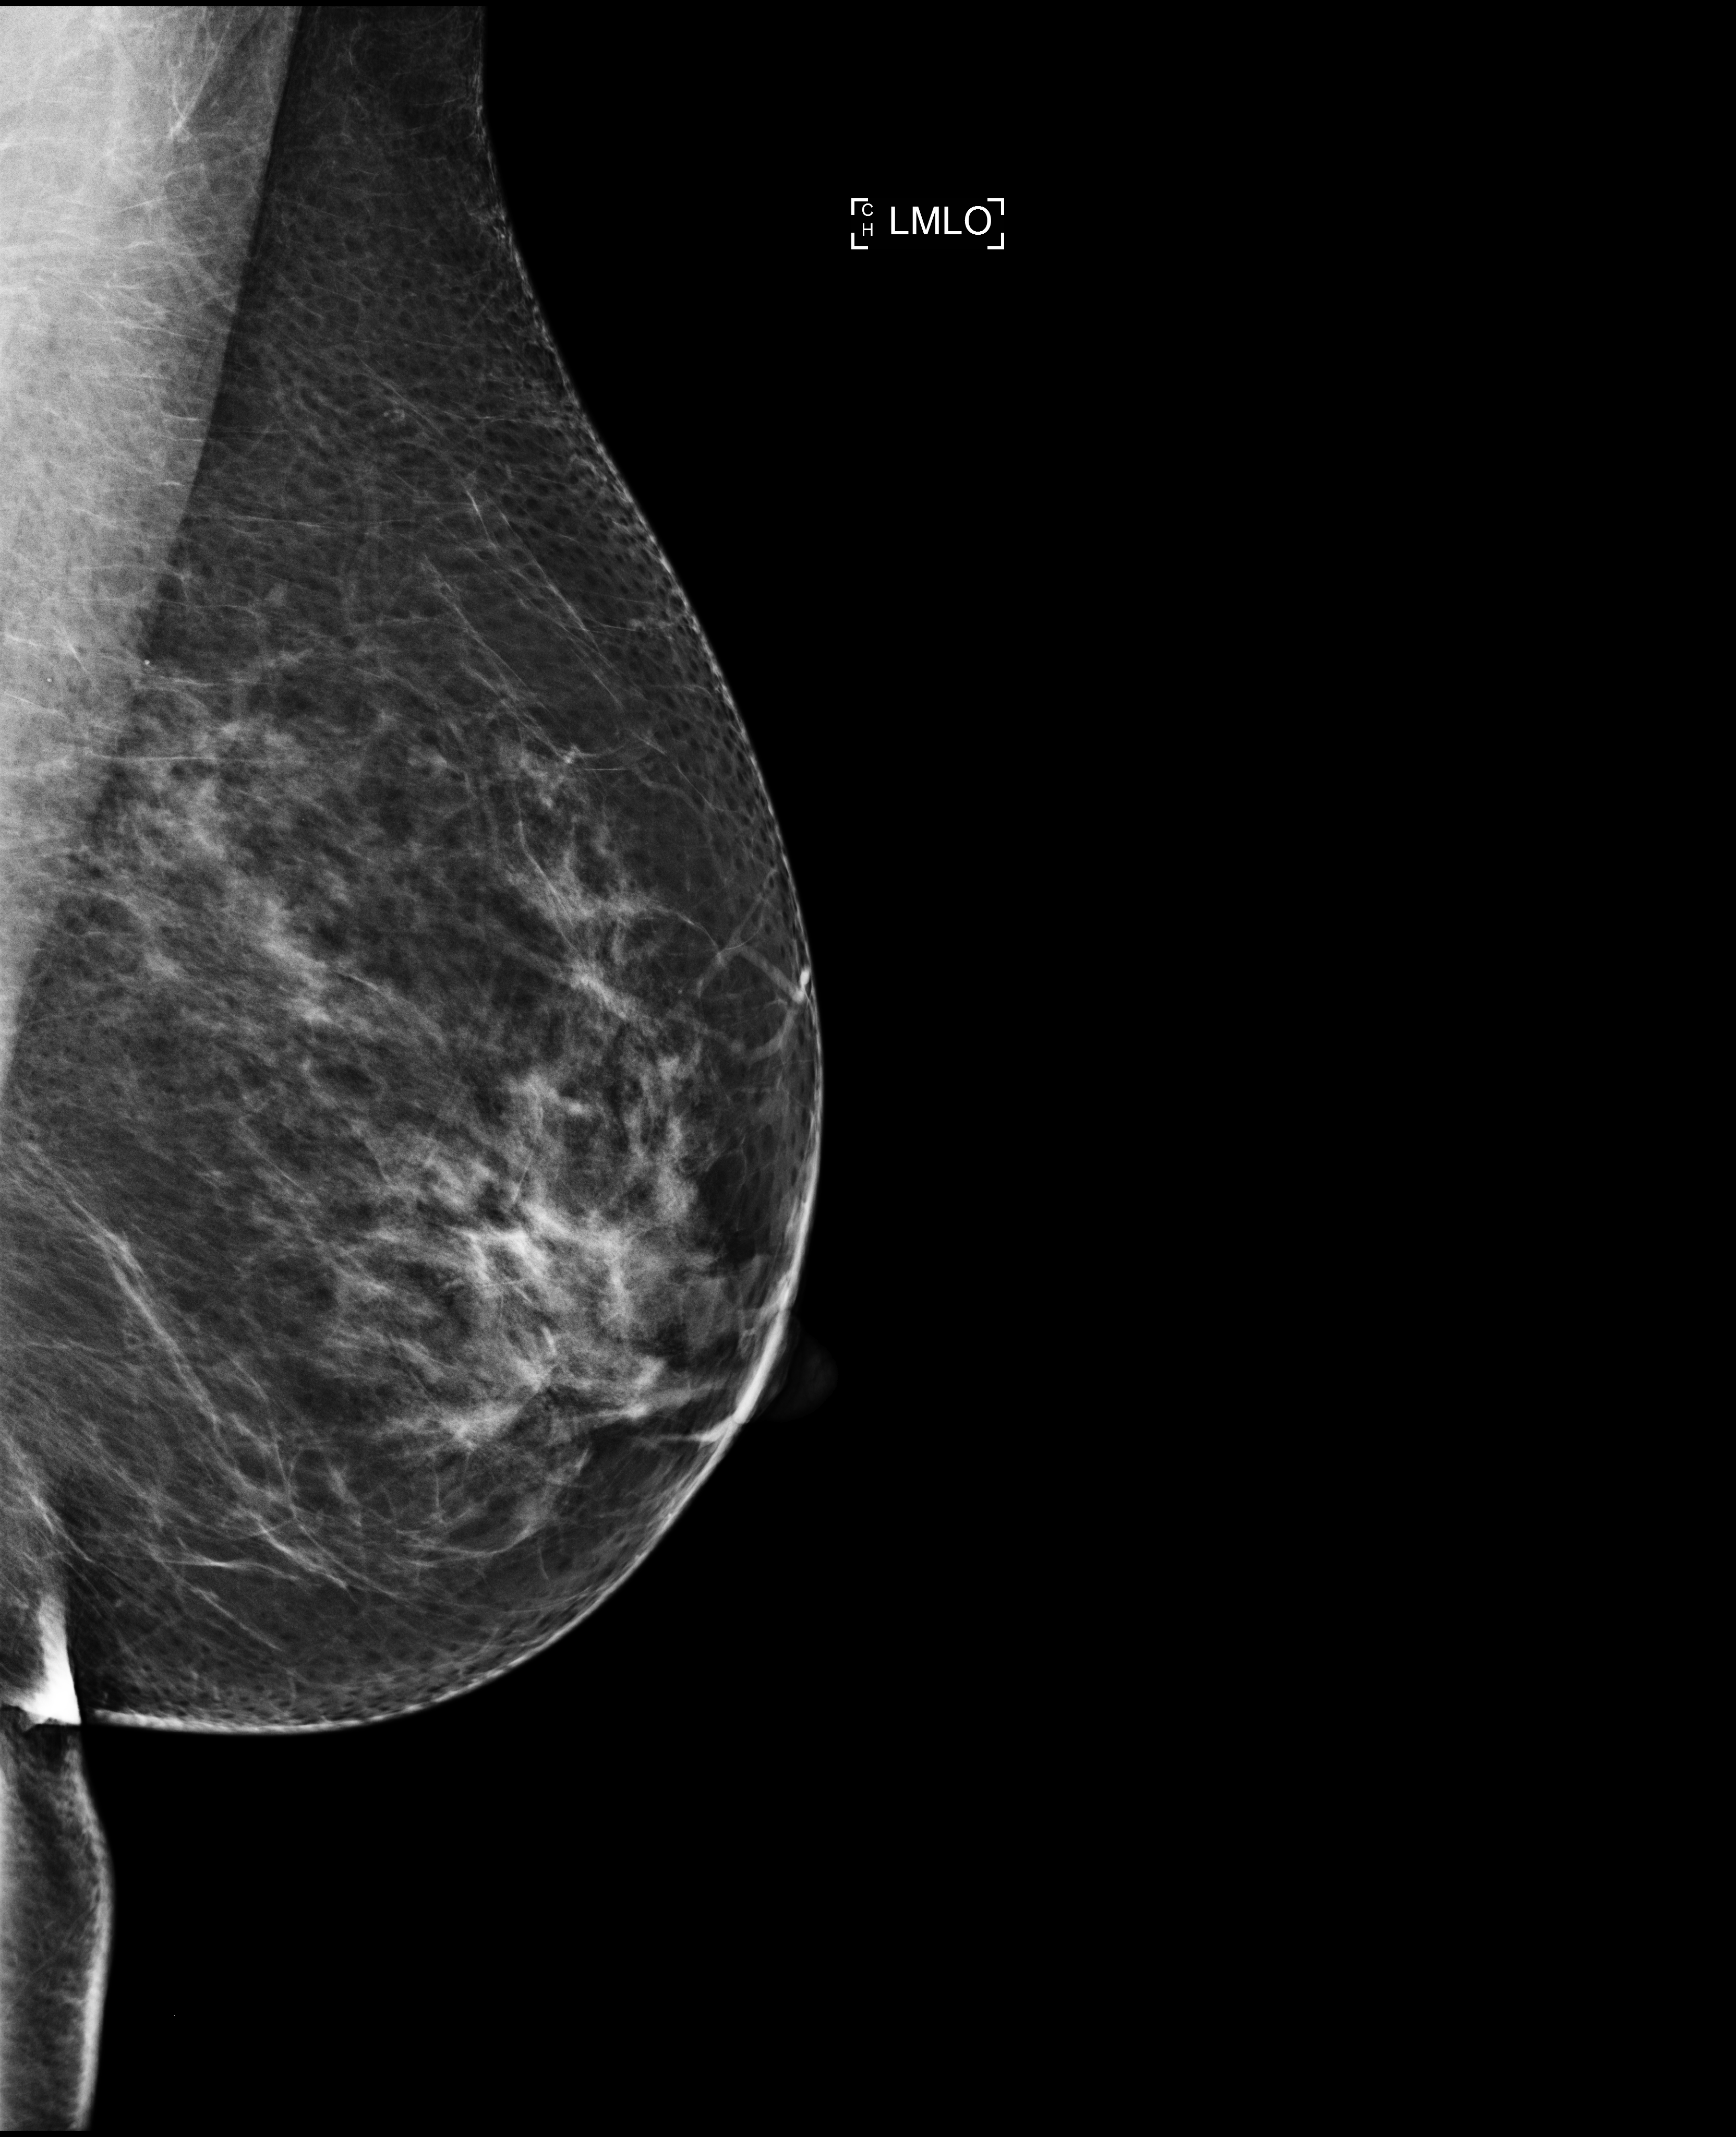
Digital mammogram (FFDM), left breast, medio-lateral oblique projection, screening examination, compressed breast thickness 88 mm, system: Selenia Dimensions. Patient: female, 49 years.
Breast density at the screening exam (both breasts): heterogeneously dense (BI-RADS density category c). Final BI-RADS assessment for this screening round (tomosynthesis exam, both breasts): category 1. Recall: no recall after this screen.